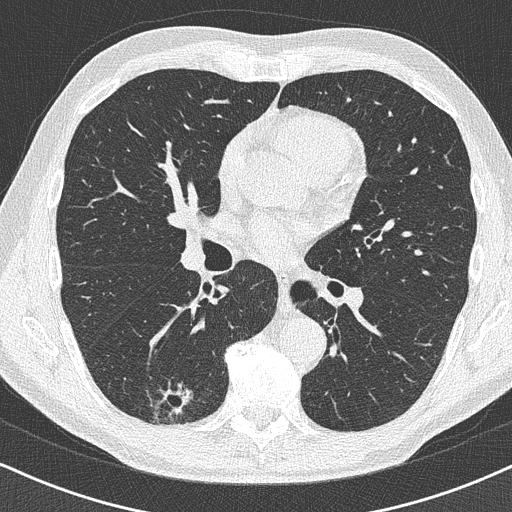
Low-dose screening chest CT, one axial slice; position 231 of 438 along the scan axis; reconstruction kernel B50f; 120 kVp; lung window (W 1500 / L -600 HU); 512 × 512 image matrix, field of view 320 × 320 mm.
Annotated regions visible in this slice (expert manual segmentation):
- lesion 1 (tumor, lower lobe of right lung): bounding box (x1, y1, x2, y2) in pixels: (173, 388, 190, 416)